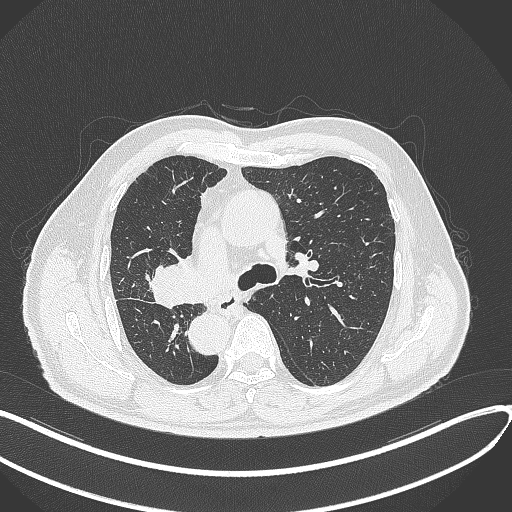
Chest CT, one axial slice. Slice 195 of 300 in the series (ordered by position). Lung window (W 1500 / L -600 HU). 1 mm slice thickness. 512 × 512 image matrix, field of view 400 × 400 mm. Patient: male, 67 years. Case-level facts recorded for this patient, not image findings: clinical TNM (as recorded): T2a N0 M0.
Outlined on this slice (bounding box drawn by a radiologist):
- lung tumour (recorded histology: squamous cell carcinoma): bounding box [x1, y1, x2, y2] px = [149, 246, 199, 309]